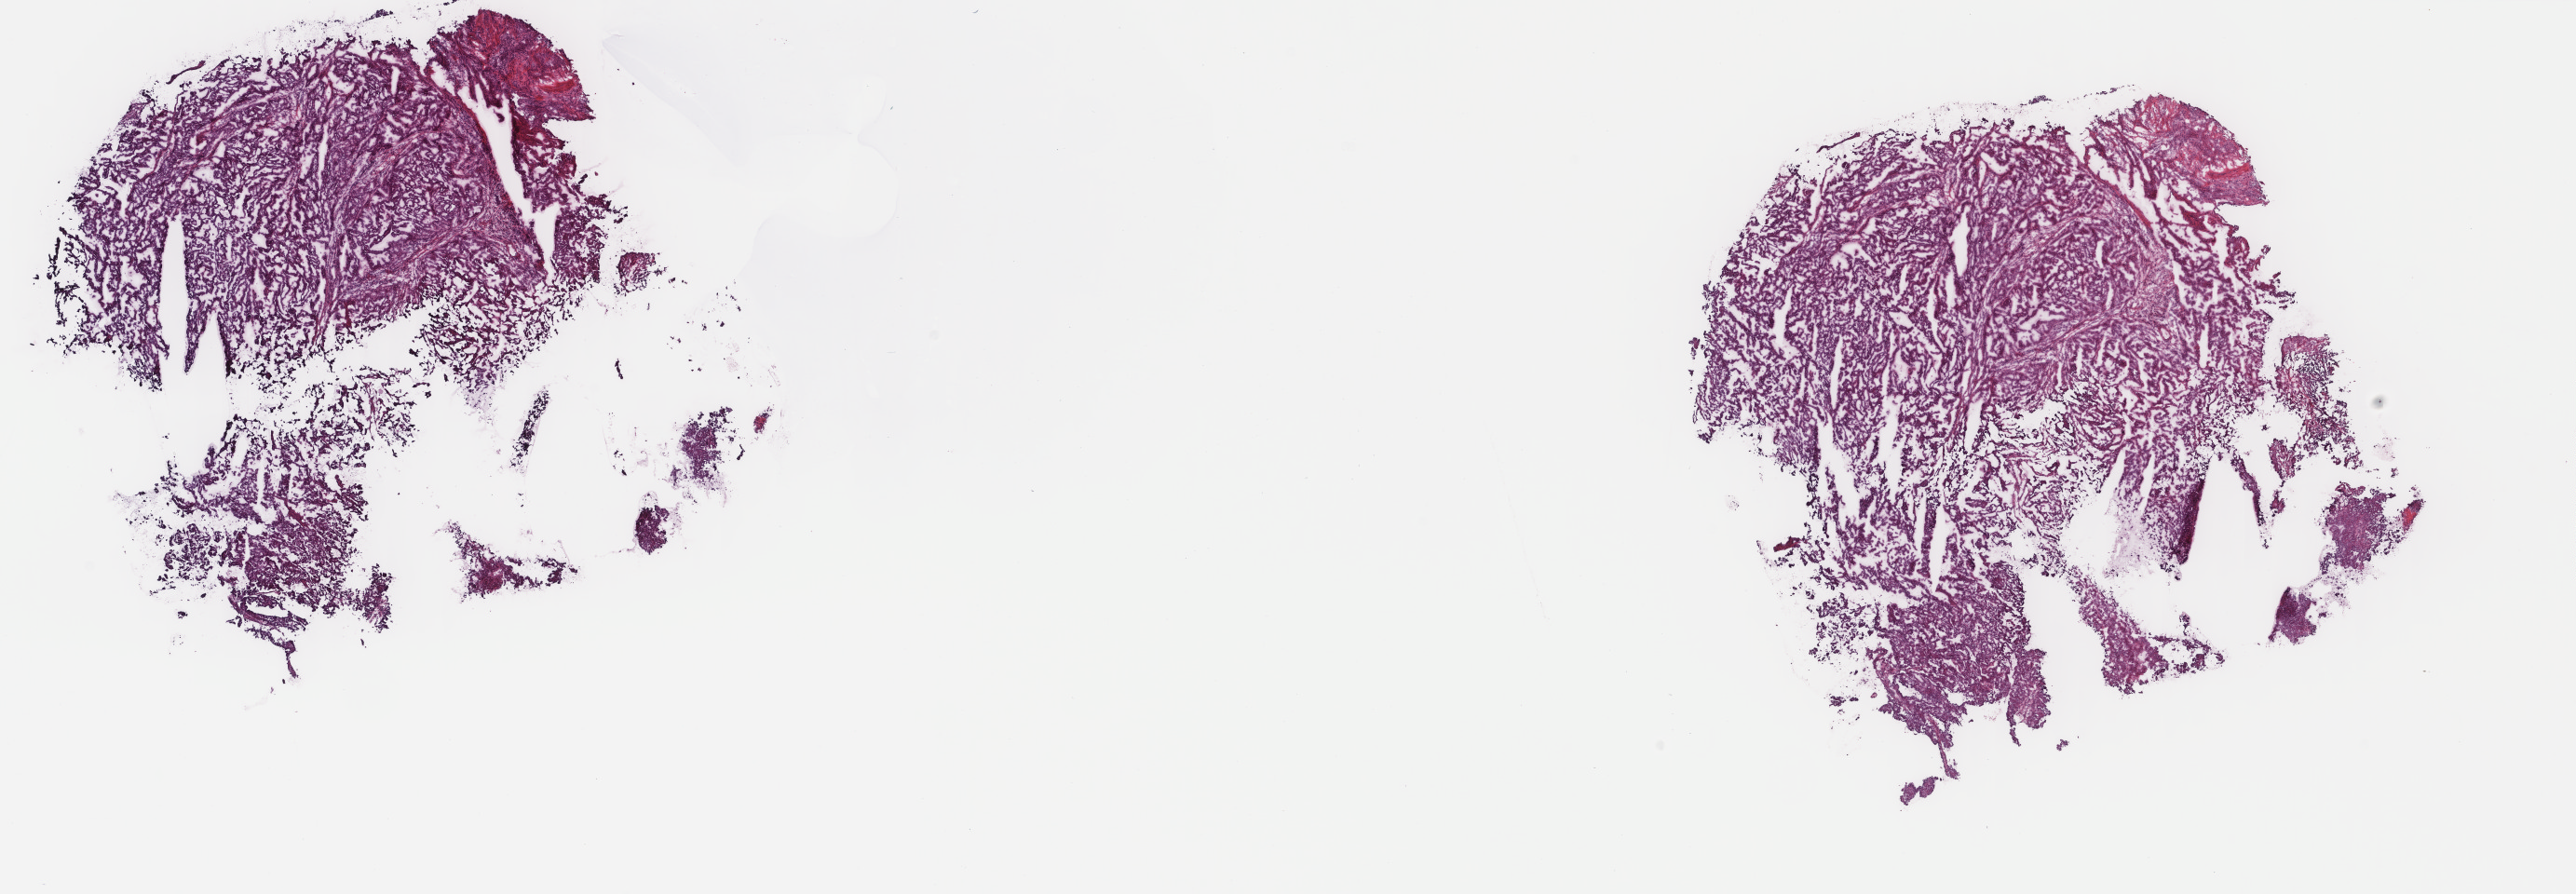
Digitized H&E-stained tissue section (whole slide) — shown as a low-resolution overview of the whole scanned area (about 22.0 x 7.6 mm, from a 40x scan). Frozen section. Uterus, primary tumour sample. Female patient; age at initial diagnosis 55 years. Histologic grade: G1 (well differentiated). Pathologist review of this section (percent, as recorded): tumour cells 100%, tumour nuclei 80%, normal cells 0%, stromal cells 0%, necrosis 0%. Infiltration values recorded for this section: lymphocyte infiltration 2%, monocyte infiltration 0%, neutrophil infiltration 0%.
* histologic diagnosis: Serous cystadenocarcinoma, NOS (endometrium)
* FIGO stage: IA